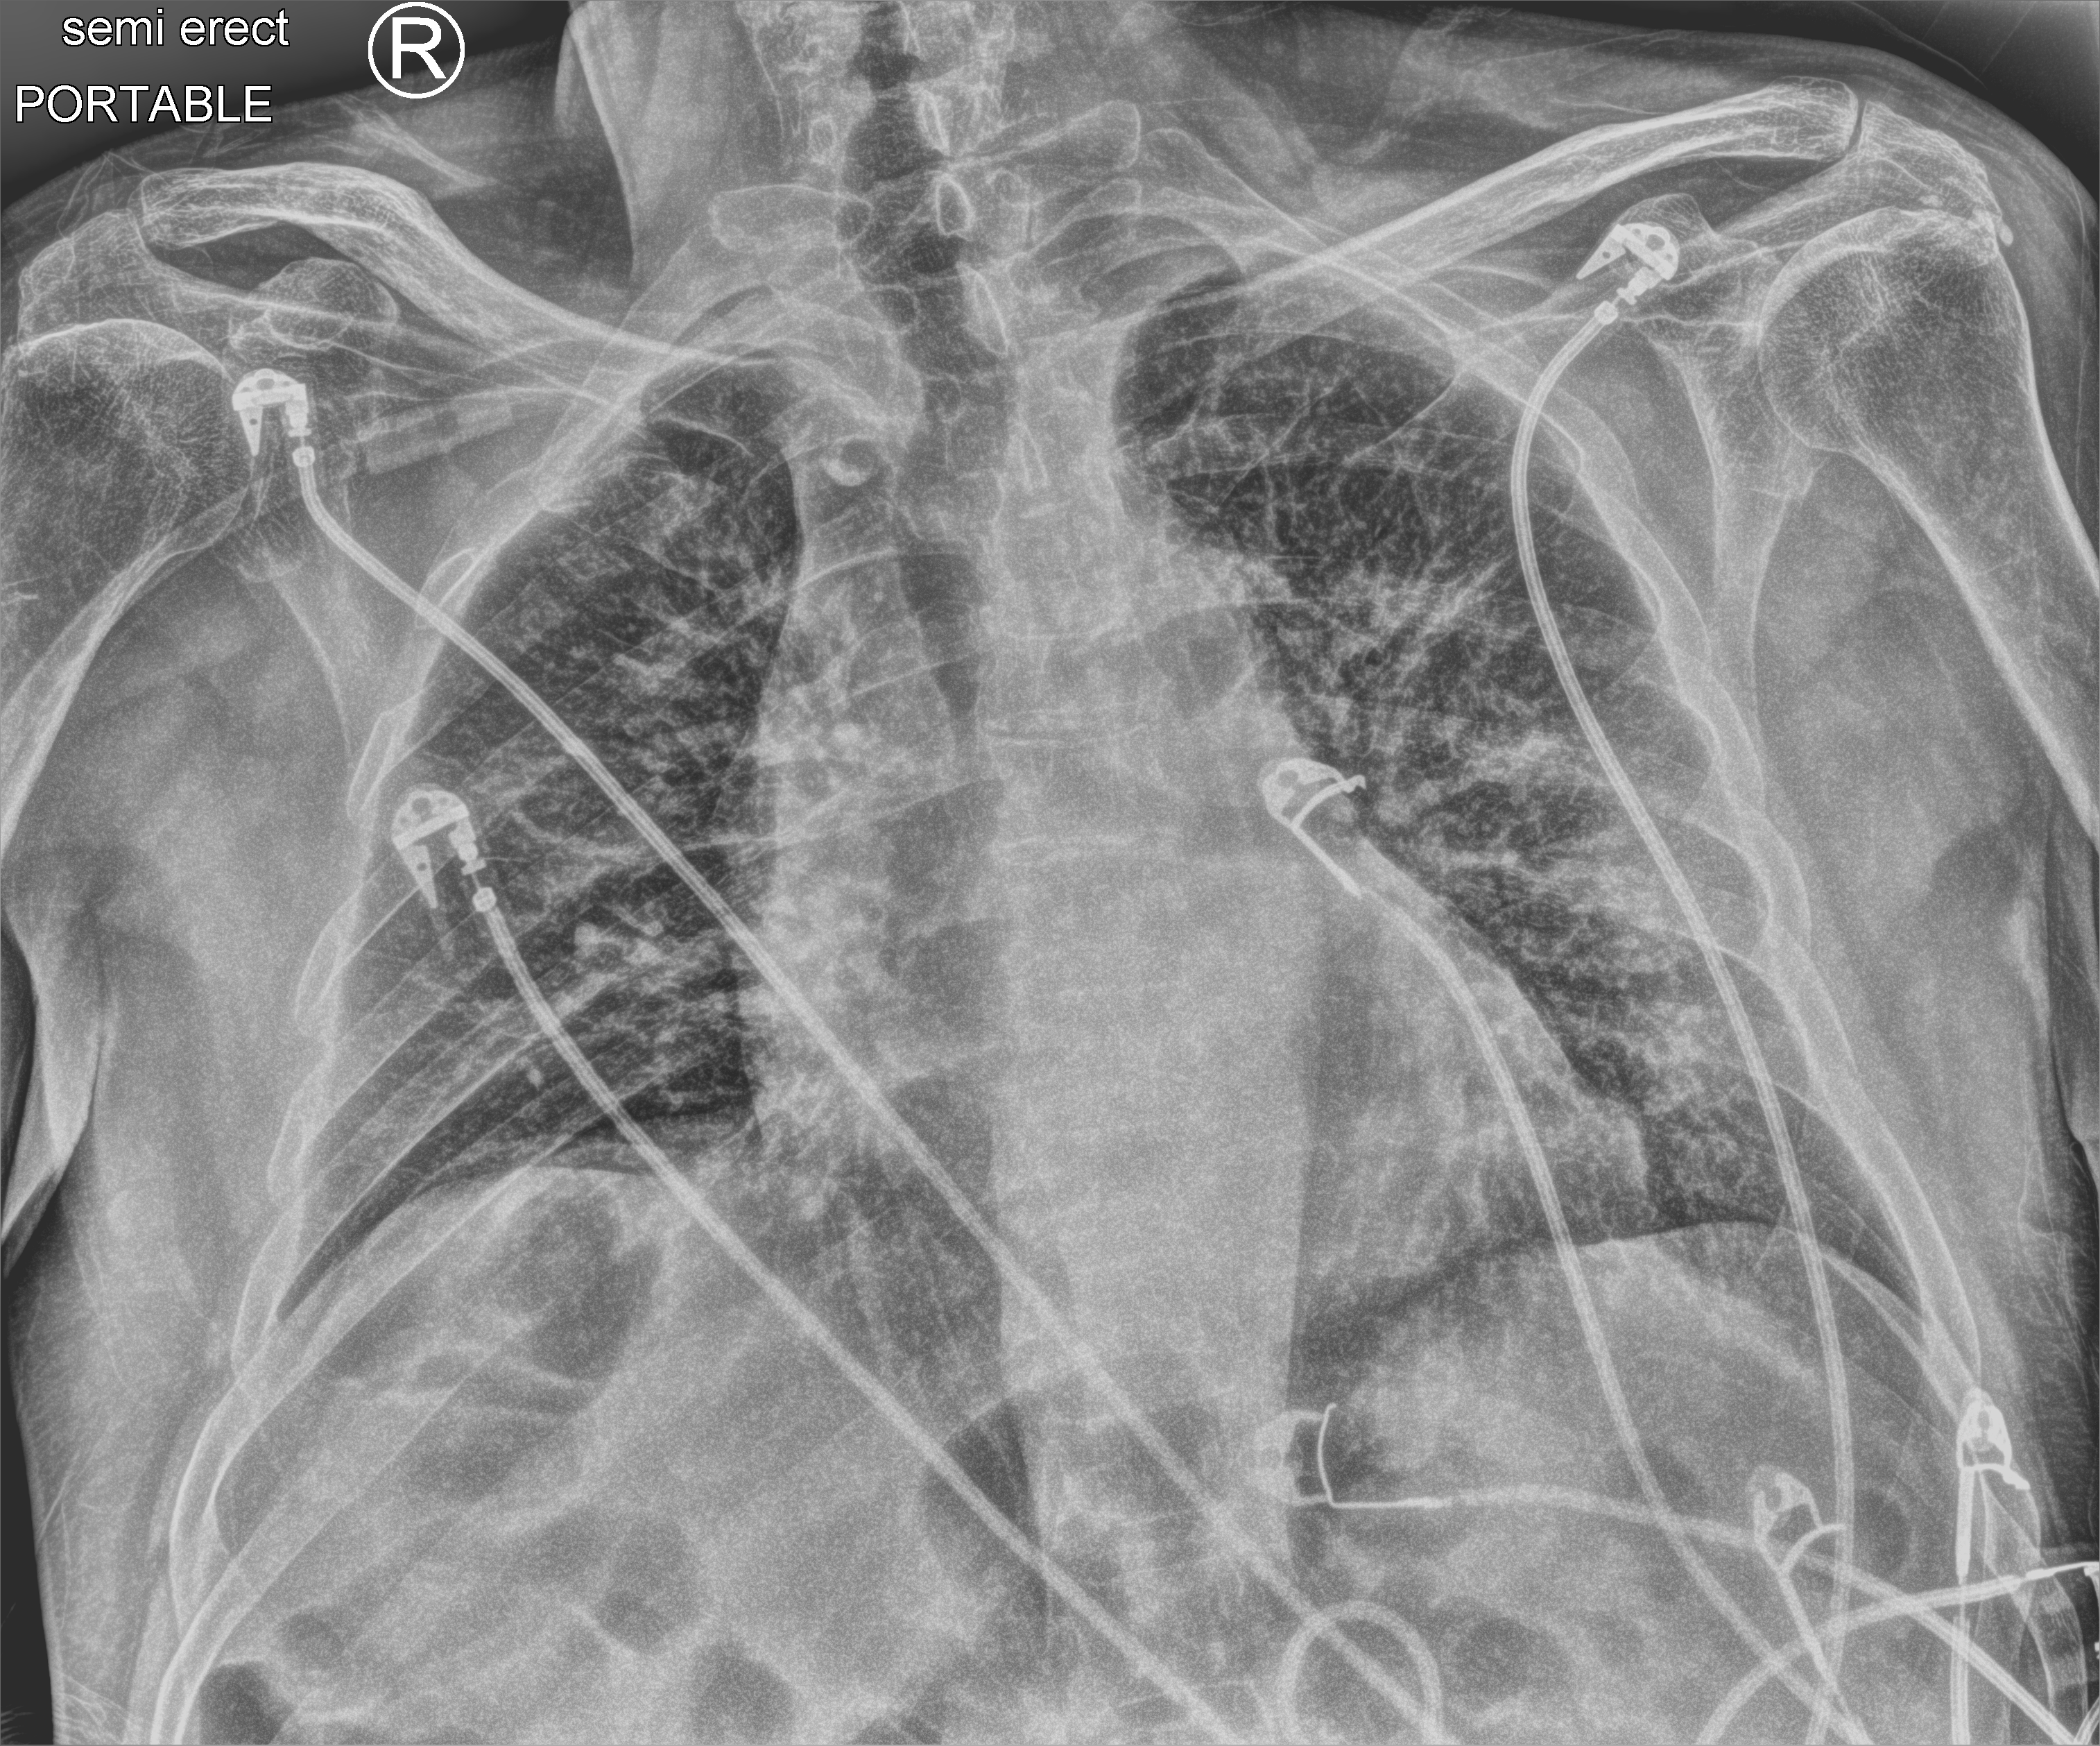
Portable chest radiograph; anteroposterior (AP) projection. Patient hospitalised with COVID-19; male, aged 60–74 years.
From the hospital-stay record, not from the radiograph (when in the stay this image was taken is not recorded):
- admitted to intensive care during this hospital stay: yes